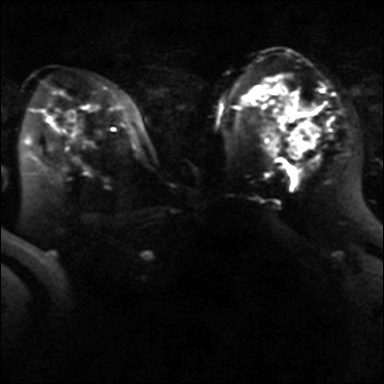
Breast MRI, one axial slice; position 23 of 40 along the scan axis; diffusion-weighted series; image 2 of 4 stored at this slice position (different b-values; order by instance number); 3 T; 4 mm slice thickness; 384 × 384 image matrix, field of view 320 × 320 mm. Female patient.
Outlined on this slice (expert manual segmentation):
- tumour on diffusion-weighted imaging: bounding box (x1, y1, x2, y2) in pixels: (289, 122, 318, 154)